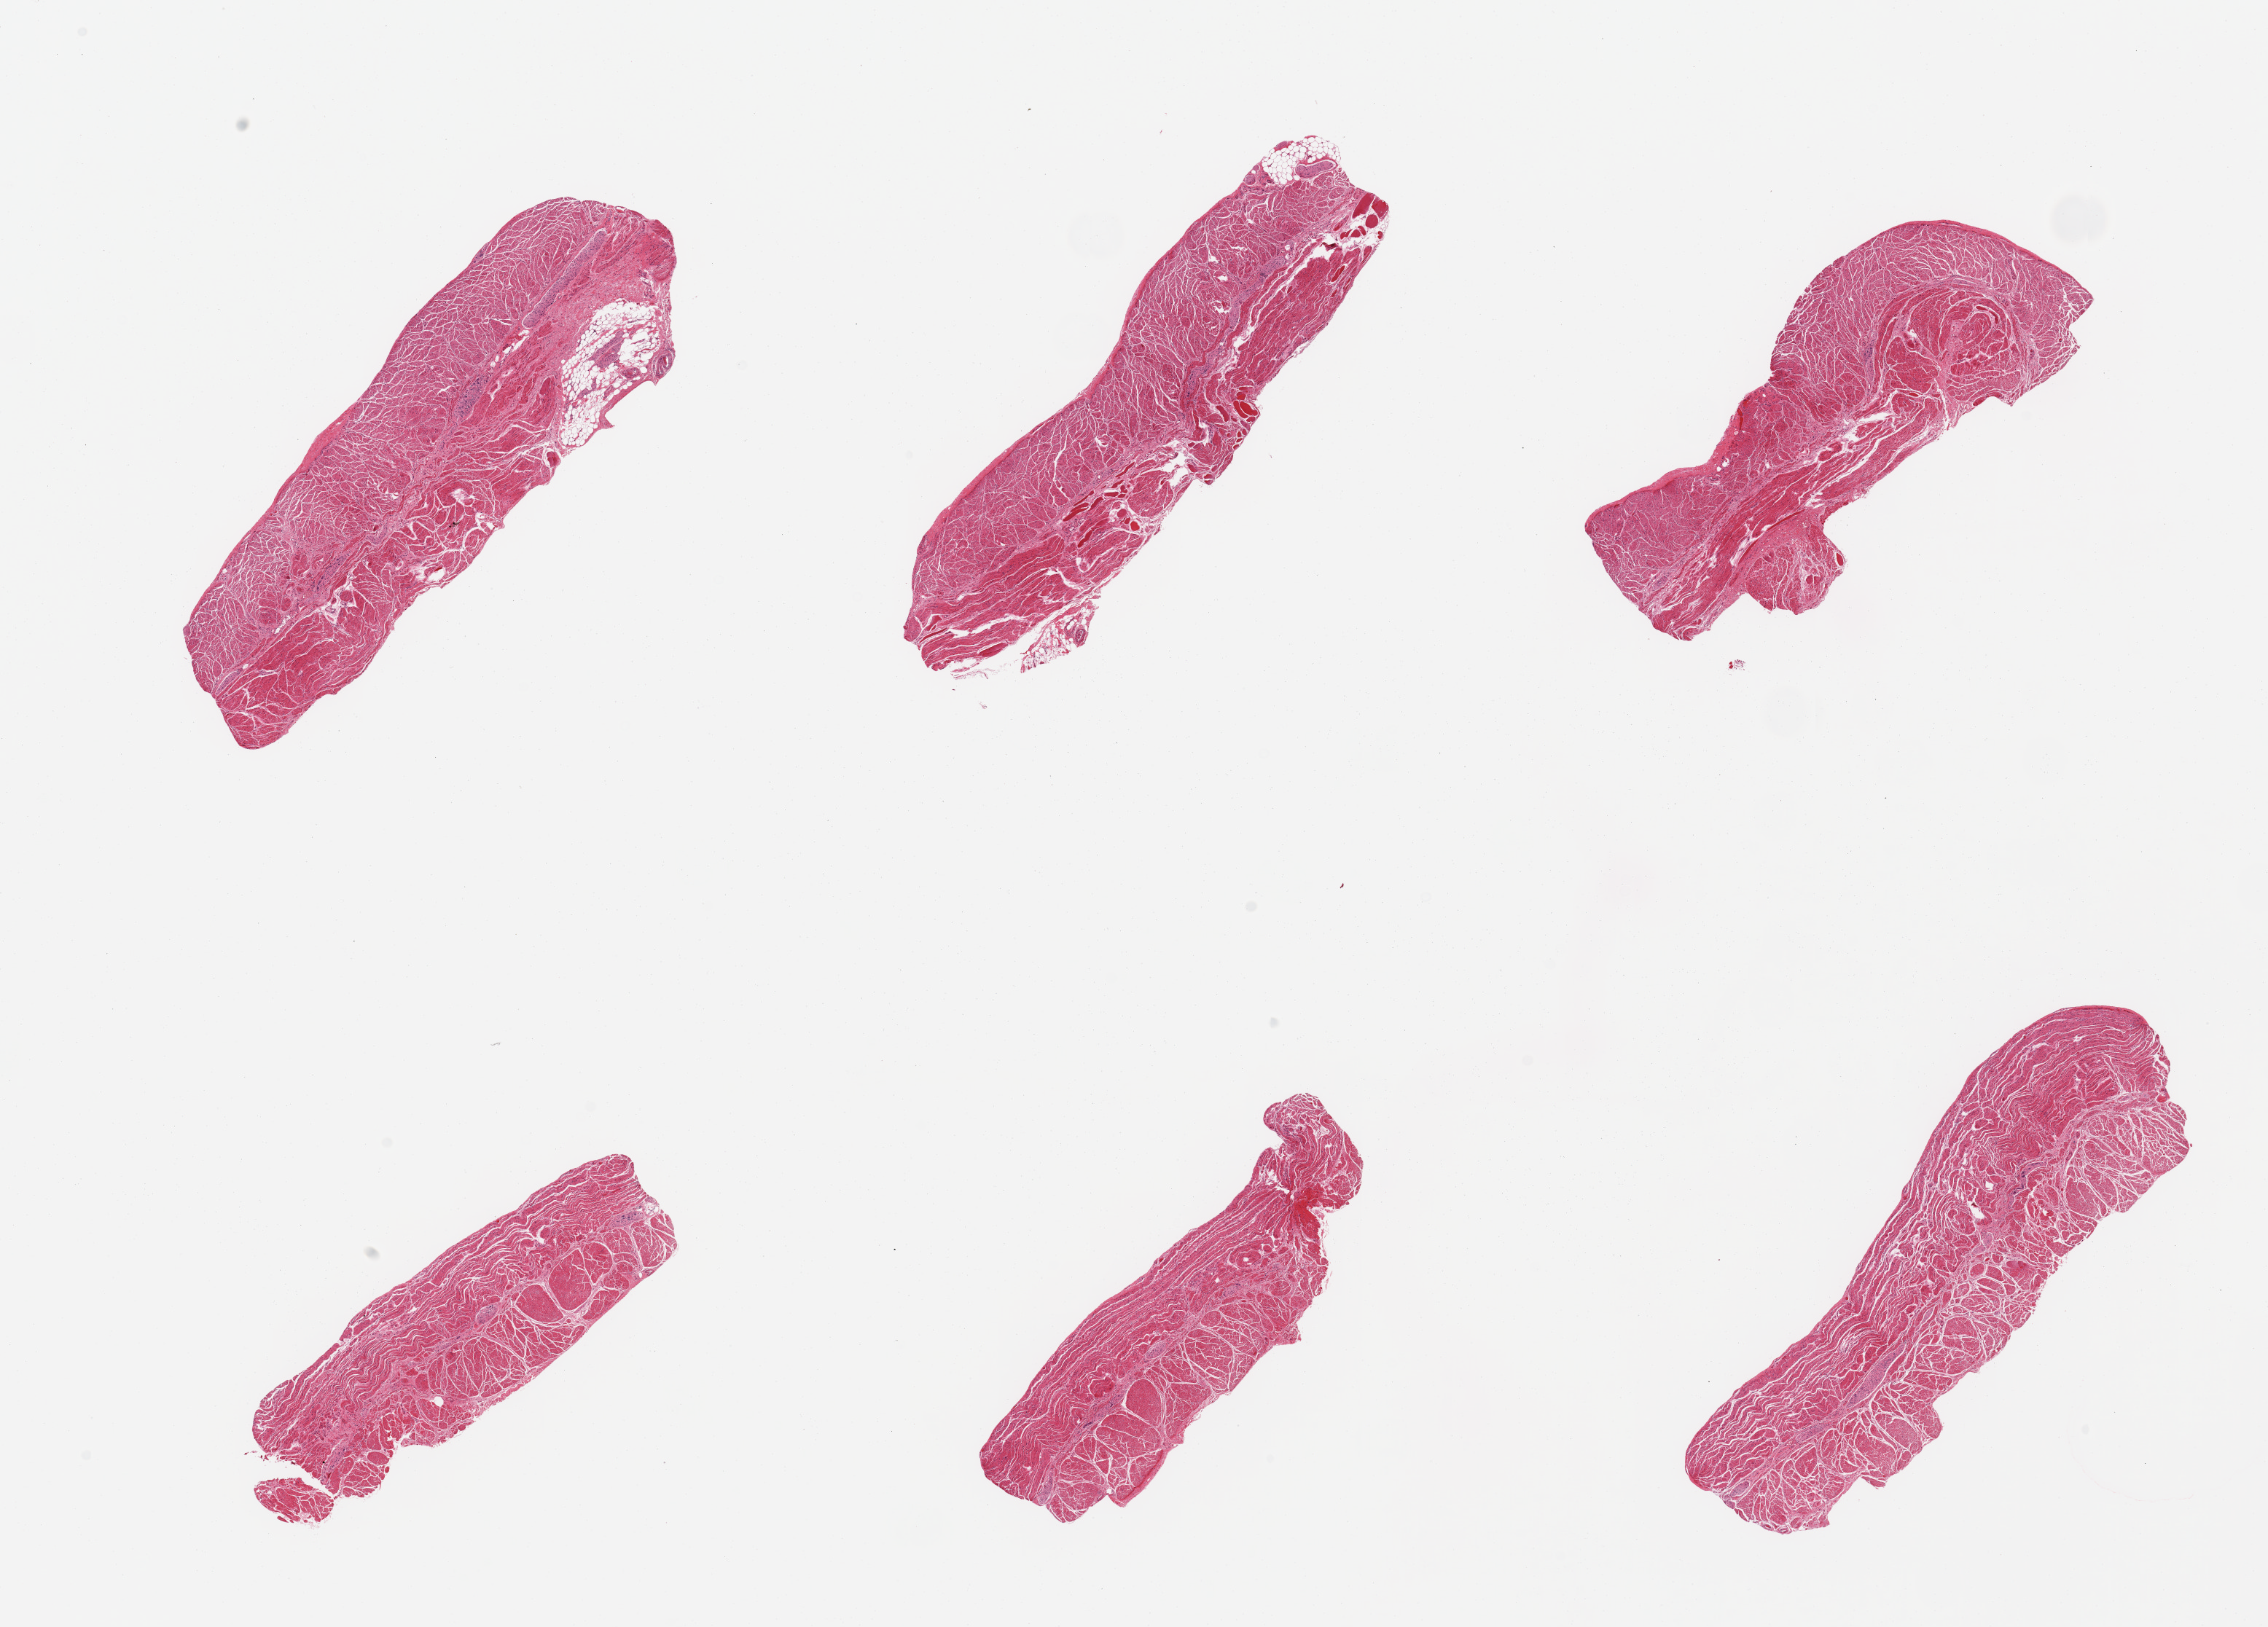
Digitized hematoxylin and eosin (H&E)-stained section, low-resolution overview of the scanned area, about 24.6 x 17.7 mm, PAXgene-fixed, paraffin-embedded tissue, sampled site (target tissue): esophageal muscle, donor tissue sample.
Reviewer comment on this tissue sample: 6 pieces, all muscularis, good specimens.